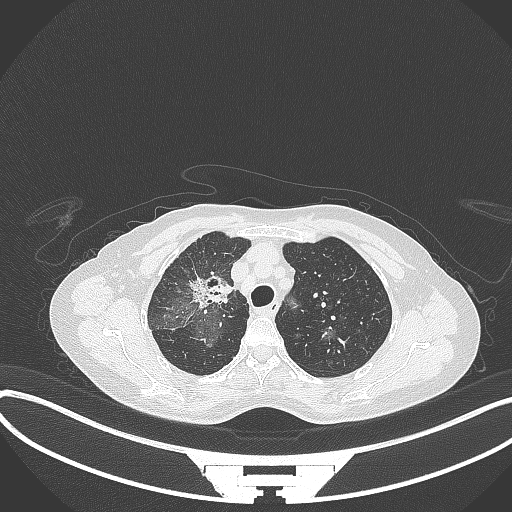
Chest CT, one axial slice; position 245 of 284 along the scan axis; 120 kVp; lung window (W 1500 / L -600 HU); 1 mm slice thickness; 512 × 512 image matrix, field of view 400 × 400 mm. Female patient, age 59 years. Case-level facts recorded for this patient, not image findings: clinical TNM (as recorded): T3 N0 M0.
Outlined on this slice (rectangle marked by the reading radiologist):
- lung tumour (recorded histology: adenocarcinoma): bounding box <184,268,240,314> (left, top, right, bottom; pixels)